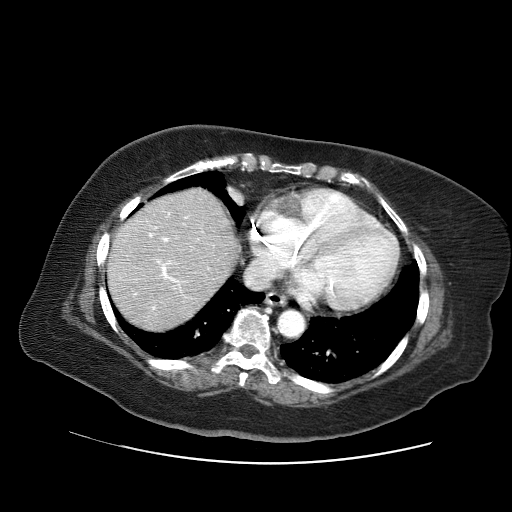
Contrast-enhanced abdominal CT (liver protocol), one axial slice; slice 58 of 71 in the series (ordered by position); reconstruction kernel STANDARD; 120 kVp; soft-tissue window (W 400 / L 40 HU); 2.5 mm slice thickness; 512 × 512 image matrix, field of view 400 × 400 mm. Case-level facts recorded for this patient, not image findings: diagnosis: hepatocellular carcinoma (patient treated with transarterial chemoembolisation; whether this scan precedes or follows treatment is not stated here); TNM stage (as recorded): Stage-II; Child-Pugh class: A; tumour differentiation: poorly differentiated; tumour nodularity: multinodular.
Outlined on this slice (semi-automatic segmentation, software-assisted and operator-edited):
- liver parenchyma outside the tumour (the mass and vessels are separate outlines, so this box may not span the whole liver): bounding box (x1, y1, x2, y2) in pixels: (108, 188, 238, 330)
- liver vessels: (135, 212, 209, 310)